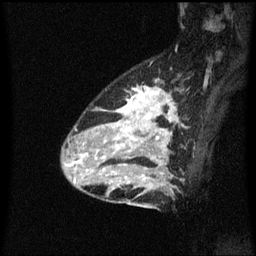
Breast MRI (dynamic contrast-enhanced), one sagittal slice. Position 43 of 60 along the scan axis. Dynamic contrast-enhanced series, image 2 of 3 at this slice position (ordered by acquisition). 1.5 T. TE 4.2 ms, TR 8.4 ms. 2 mm slice thickness. 256 × 256 image matrix, field of view 200 × 200 mm. Female patient, age 34 years. From the clinical record (not read from this slice): setting: breast cancer imaged before/during neoadjuvant chemotherapy; receptor status: HR-positive, HER2-negative.
Outlined on this slice (semi-automatically segmented with operator editing):
- analysis volume of interest (the breast-tissue region the enhancement analysis was run in; not a lesion): box from (x=69, y=88) to (x=177, y=209) px
- tumour enhancement mask (voxels above the 70 % enhancement threshold inside the analysis volume of interest): (x=74, y=88)–(x=175, y=189)